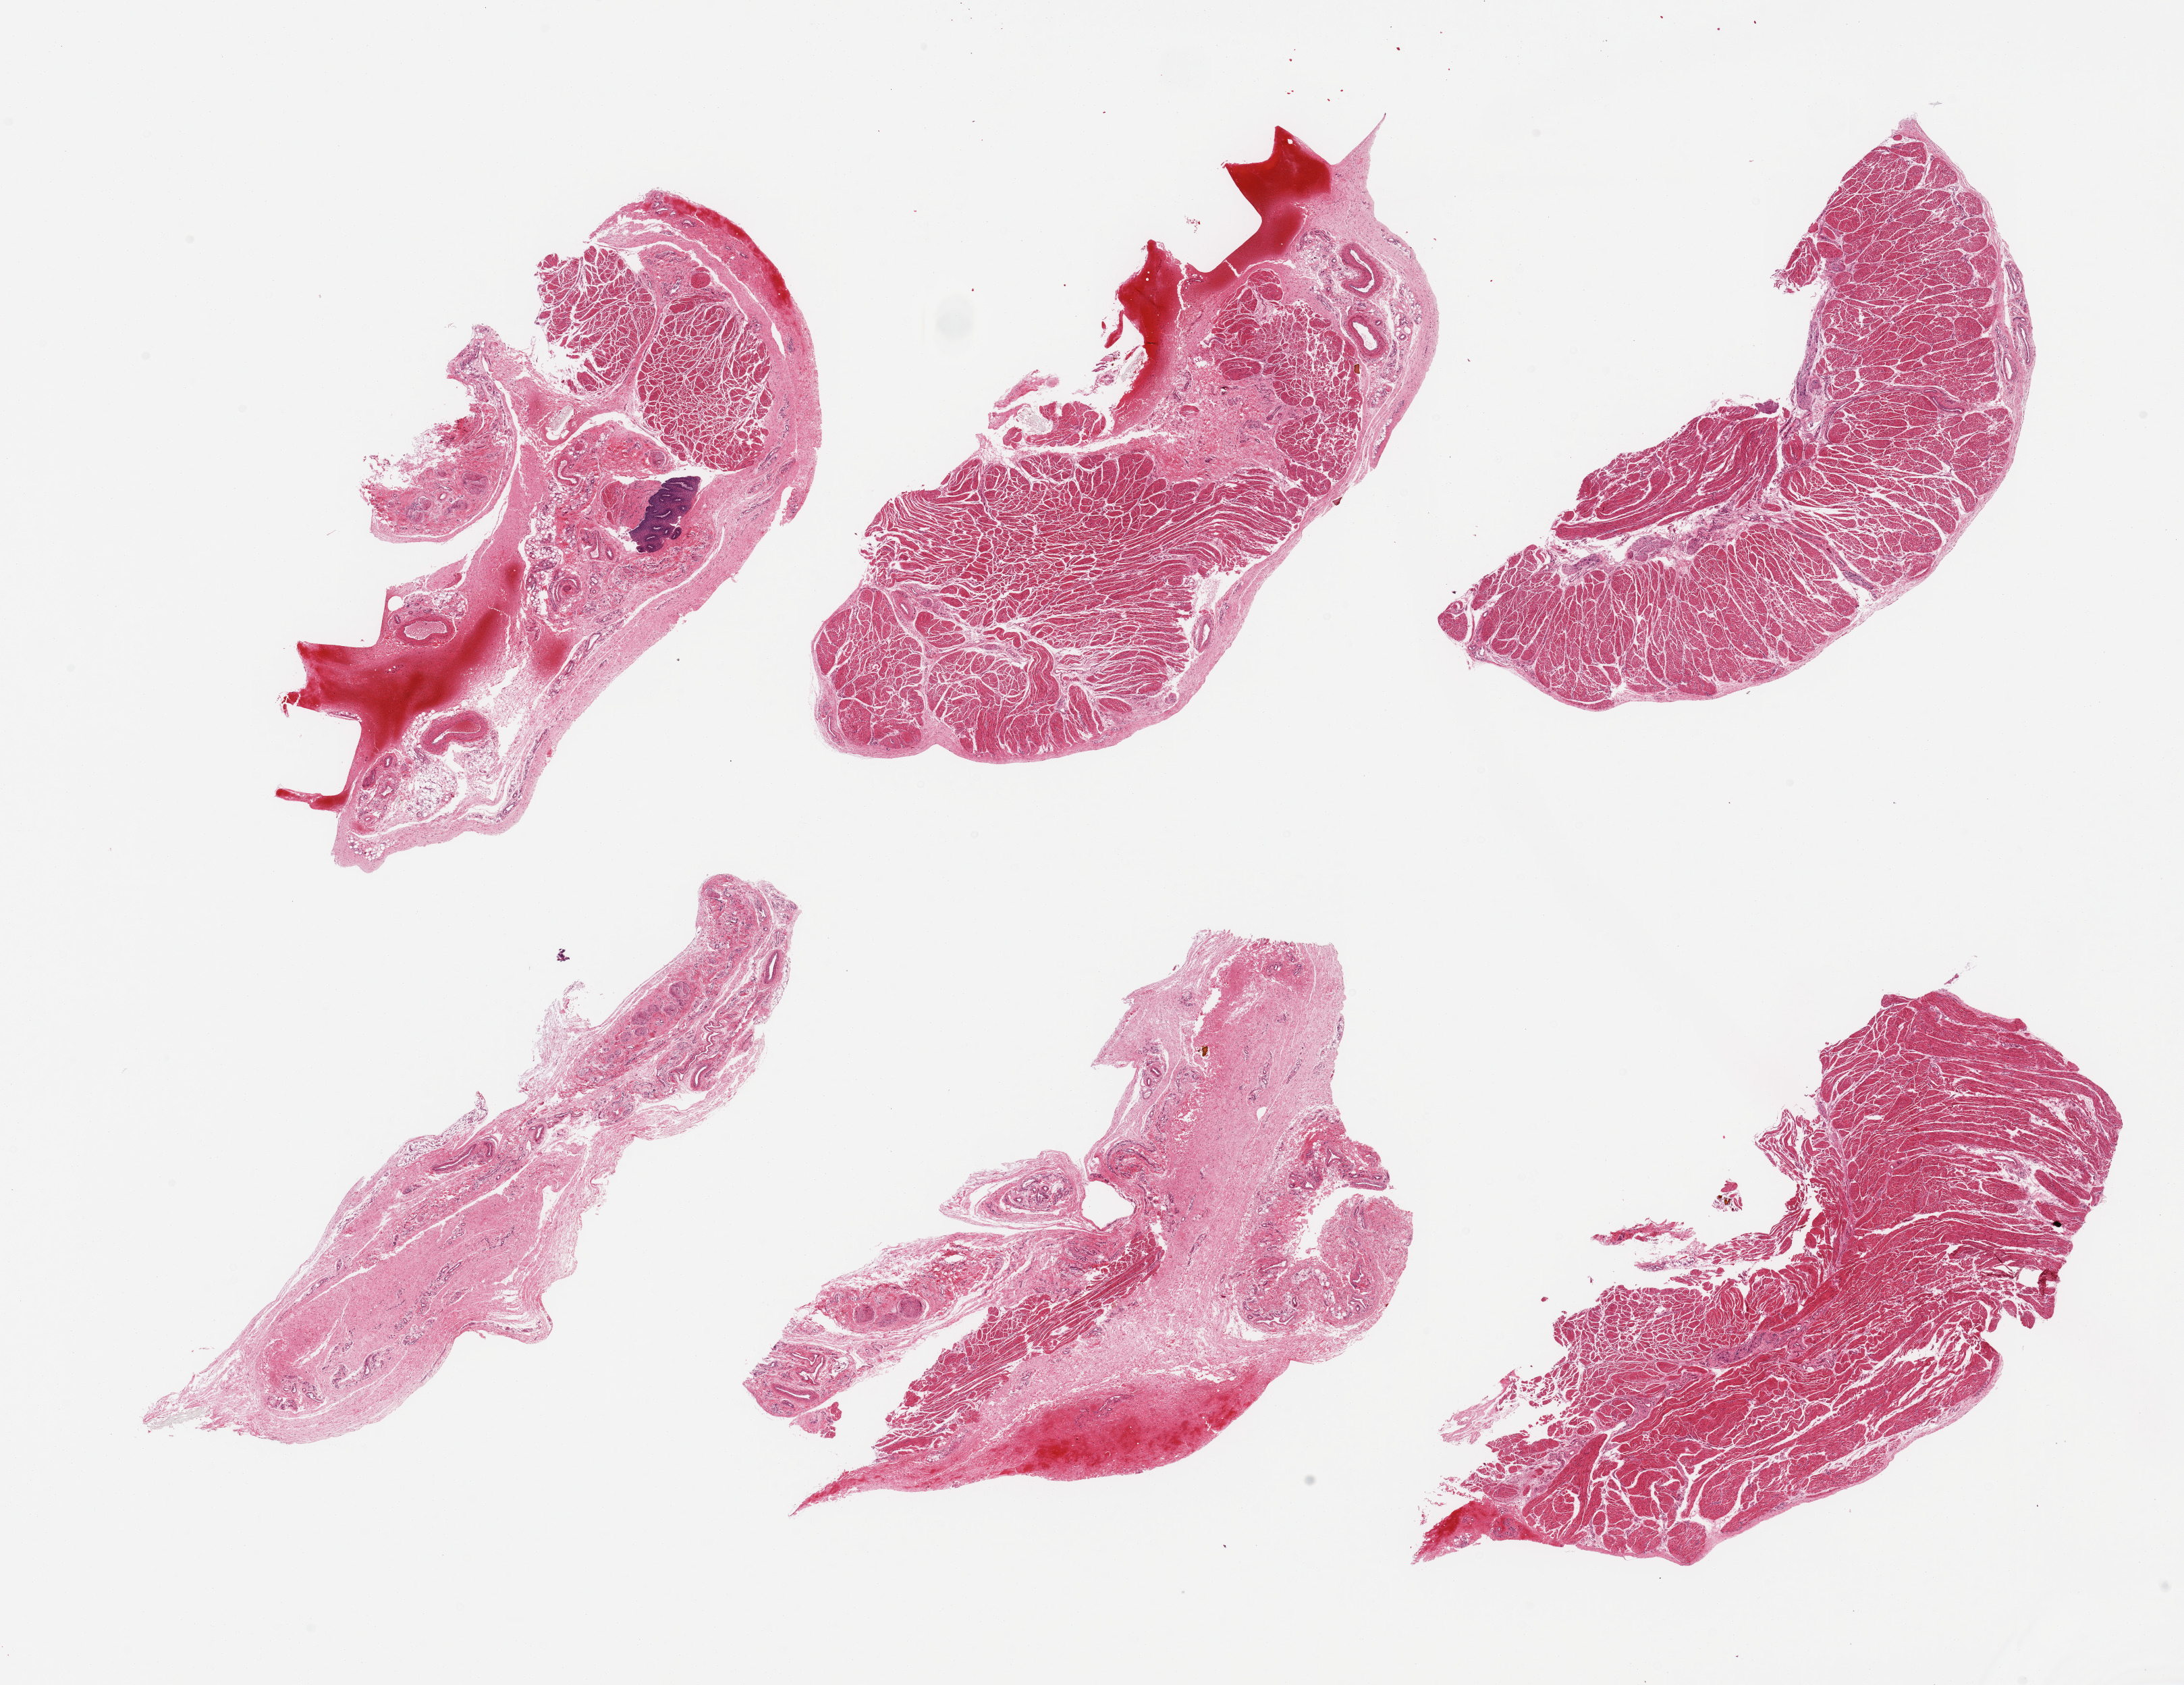
Haematoxylin and eosin whole-slide image, brightfield, low-resolution overview of the scanned area, about 25.6 x 19.7 mm (slide scanned at 20x), PAXgene-fixed paraffin-embedded (PFPE) section, section of esophageal muscle (target tissue), tissue donor sample.
* reviewer comment on this tissue sample: 6 pieces; 2 pieces are pure muscularis, 4 have 100%, 80%, 70% & 20% submucosal stroma; 1 has 1 mm squamous carry-over